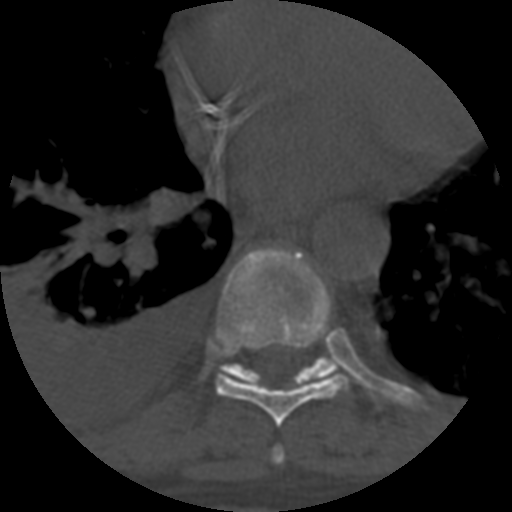
CT including the spine, one axial slice; slice 391 of 708 in the series (ordered by position); 120 kVp; one of 3 acquisitions stored at this slice position; bone window (W 1800 / L 400 HU); 1.25 mm slice thickness; 512 × 512 image matrix. Patient age 55 years. From the clinical record (not read from this slice): primary cancer: colon; vertebrae with lytic lesions (as recorded): T12, L1, L5.
Structures marked on this image (semi-automatic segmentation, software-assisted and operator-edited):
- T7 vertebra: box from (x=271, y=446) to (x=285, y=465) px
- T8 vertebra: (x=215, y=249)–(x=350, y=427)
- T9 vertebra: (x=220, y=255)–(x=338, y=386)